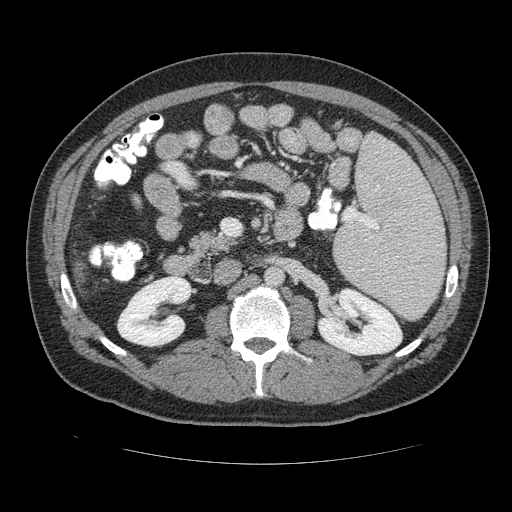
Contrast-enhanced abdominal CT (liver protocol), one axial slice; position 49 of 113 along the scan axis; 120 kVp; soft-tissue window (W 400 / L 40 HU); 512 × 512 image matrix. From the clinical record (not read from this slice): diagnosis: hepatocellular carcinoma (patient treated with transarterial chemoembolisation; whether this scan precedes or follows treatment is not stated here); TNM stage (as recorded): Stage-II; Child-Pugh class: B; tumour differentiation: moderately differentiated; tumour nodularity: multinodular.
Annotated regions visible in this slice (semi-automatically segmented with operator editing):
- liver parenchyma outside the tumour (the mass and vessels are separate outlines, so this box may not span the whole liver): bounding box <70,254,88,284> (left, top, right, bottom; pixels)